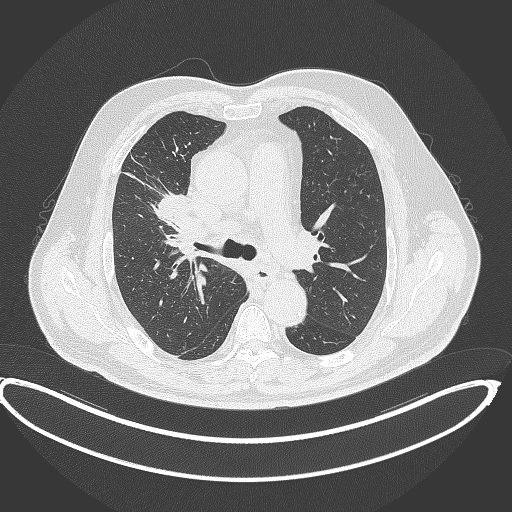
Chest CT, one axial slice. Slice 266 of 390 in the series (ordered by position). Reconstruction kernel B70f. Lung window (W 1500 / L -600 HU). 512 × 512 image matrix. Male patient, age 62 years. From the clinical record (not read from this slice): clinical TNM (as recorded): T1c N3 M1c.
Annotated regions visible in this slice (bounding box drawn by a radiologist):
- lung tumour (recorded histology: adenocarcinoma): bounding box <153,194,196,233> (left, top, right, bottom; pixels)